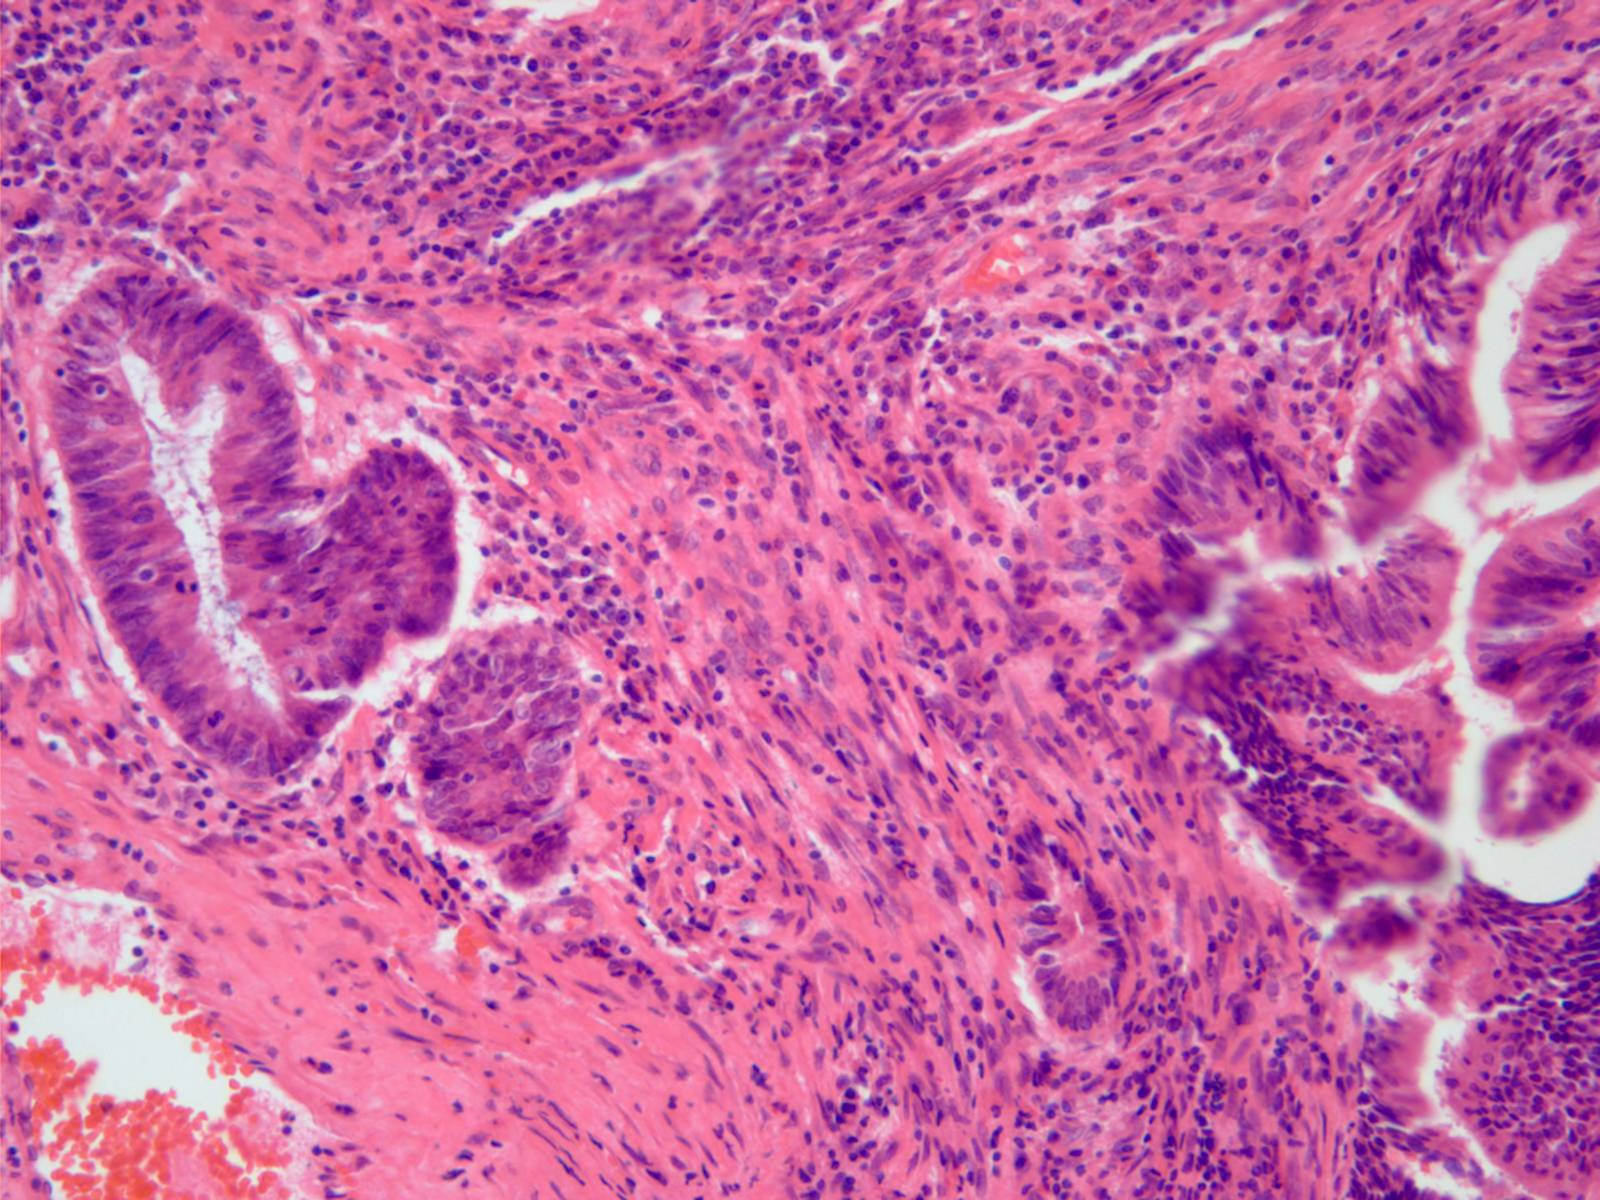
Hematoxylin and eosin (H&E) stained micrograph of a single small tissue field — covering about 0.8 x 0.6 mm; formalin-fixed paraffin-embedded (FFPE) diagnostic section; sample: primary tumour, stomach. Female, age 71 years at initial diagnosis. Histologic grade: G1 (well differentiated).
Pathologic diagnosis: Adenocarcinoma, NOS (body of stomach).